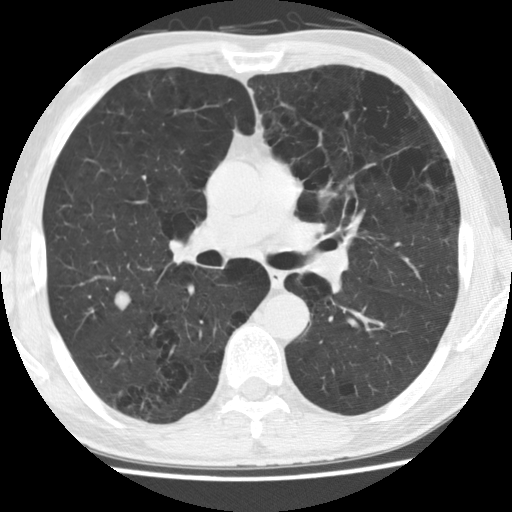
Chest CT (low-dose screening protocol), one axial image. Baseline annual screen. Lung window (W 1500 / L -600 HU). 2.5 mm slice thickness. Slice 71 of 158 in the series. Male, age 62 years at enrolment. Current smoker at enrolment.
Expert reader's lesion annotation, bounding box (x1, y1, x2, y2) in pixels: (88, 267, 147, 329). The screening reader recorded 2 non-calcified nodules or masses ≥4 mm on this exam (left upper lobe, right upper lobe); which of them this box marks is not recorded. Official screen result: positive, change unspecified: nodule(s) >= 4 mm or enlarging nodule(s), mass(es), or other non-specific abnormalities suspicious for lung cancer. Participant outcome: lung cancer diagnosed 288 days after this screen — oat cell carcinoma, right upper lobe, undifferentiated (G4), stage IV (AJCC 6th edition), 30 mm at pathology.